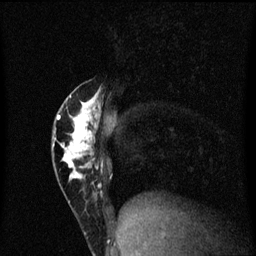
Breast MRI (dynamic contrast-enhanced), one sagittal slice. Position 23 of 60 along the scan axis. Dynamic contrast-enhanced series, image 2 of 3 at this slice position (ordered by acquisition). 1.5 T. TE 4.2 ms, TR 8.4 ms. 256 × 256 image matrix. Patient: female, 40 years.
Annotated regions visible in this slice (semi-automatic segmentation, software-assisted and operator-edited):
- analysis volume of interest (the breast-tissue region the enhancement analysis was run in; not a lesion): bounding box <53,80,106,203> (left, top, right, bottom; pixels)
- tumour enhancement mask (voxels above the 70 % enhancement threshold inside the analysis volume of interest): <53,94,104,181>